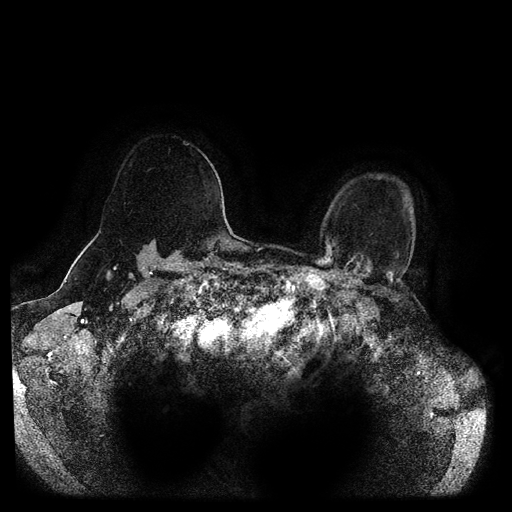
Breast MRI (dynamic contrast-enhanced, multi-phase), one axial slice; slice 83 of 116 in the series (ordered by position); dynamic contrast-enhanced series, time point 2 of 5 at this slice position (early post-contrast); 1.5 T; TE 2.6 ms, TR 5.3 ms; 2 mm slice thickness; 512 × 512 image matrix, field of view 370 × 370 mm. Patient: female, 55 years.
Annotated regions visible in this slice (semi-automatic segmentation, software-assisted and operator-edited):
- breast lesion (labelled benign in the annotation): box from (x=343, y=252) to (x=394, y=284) px